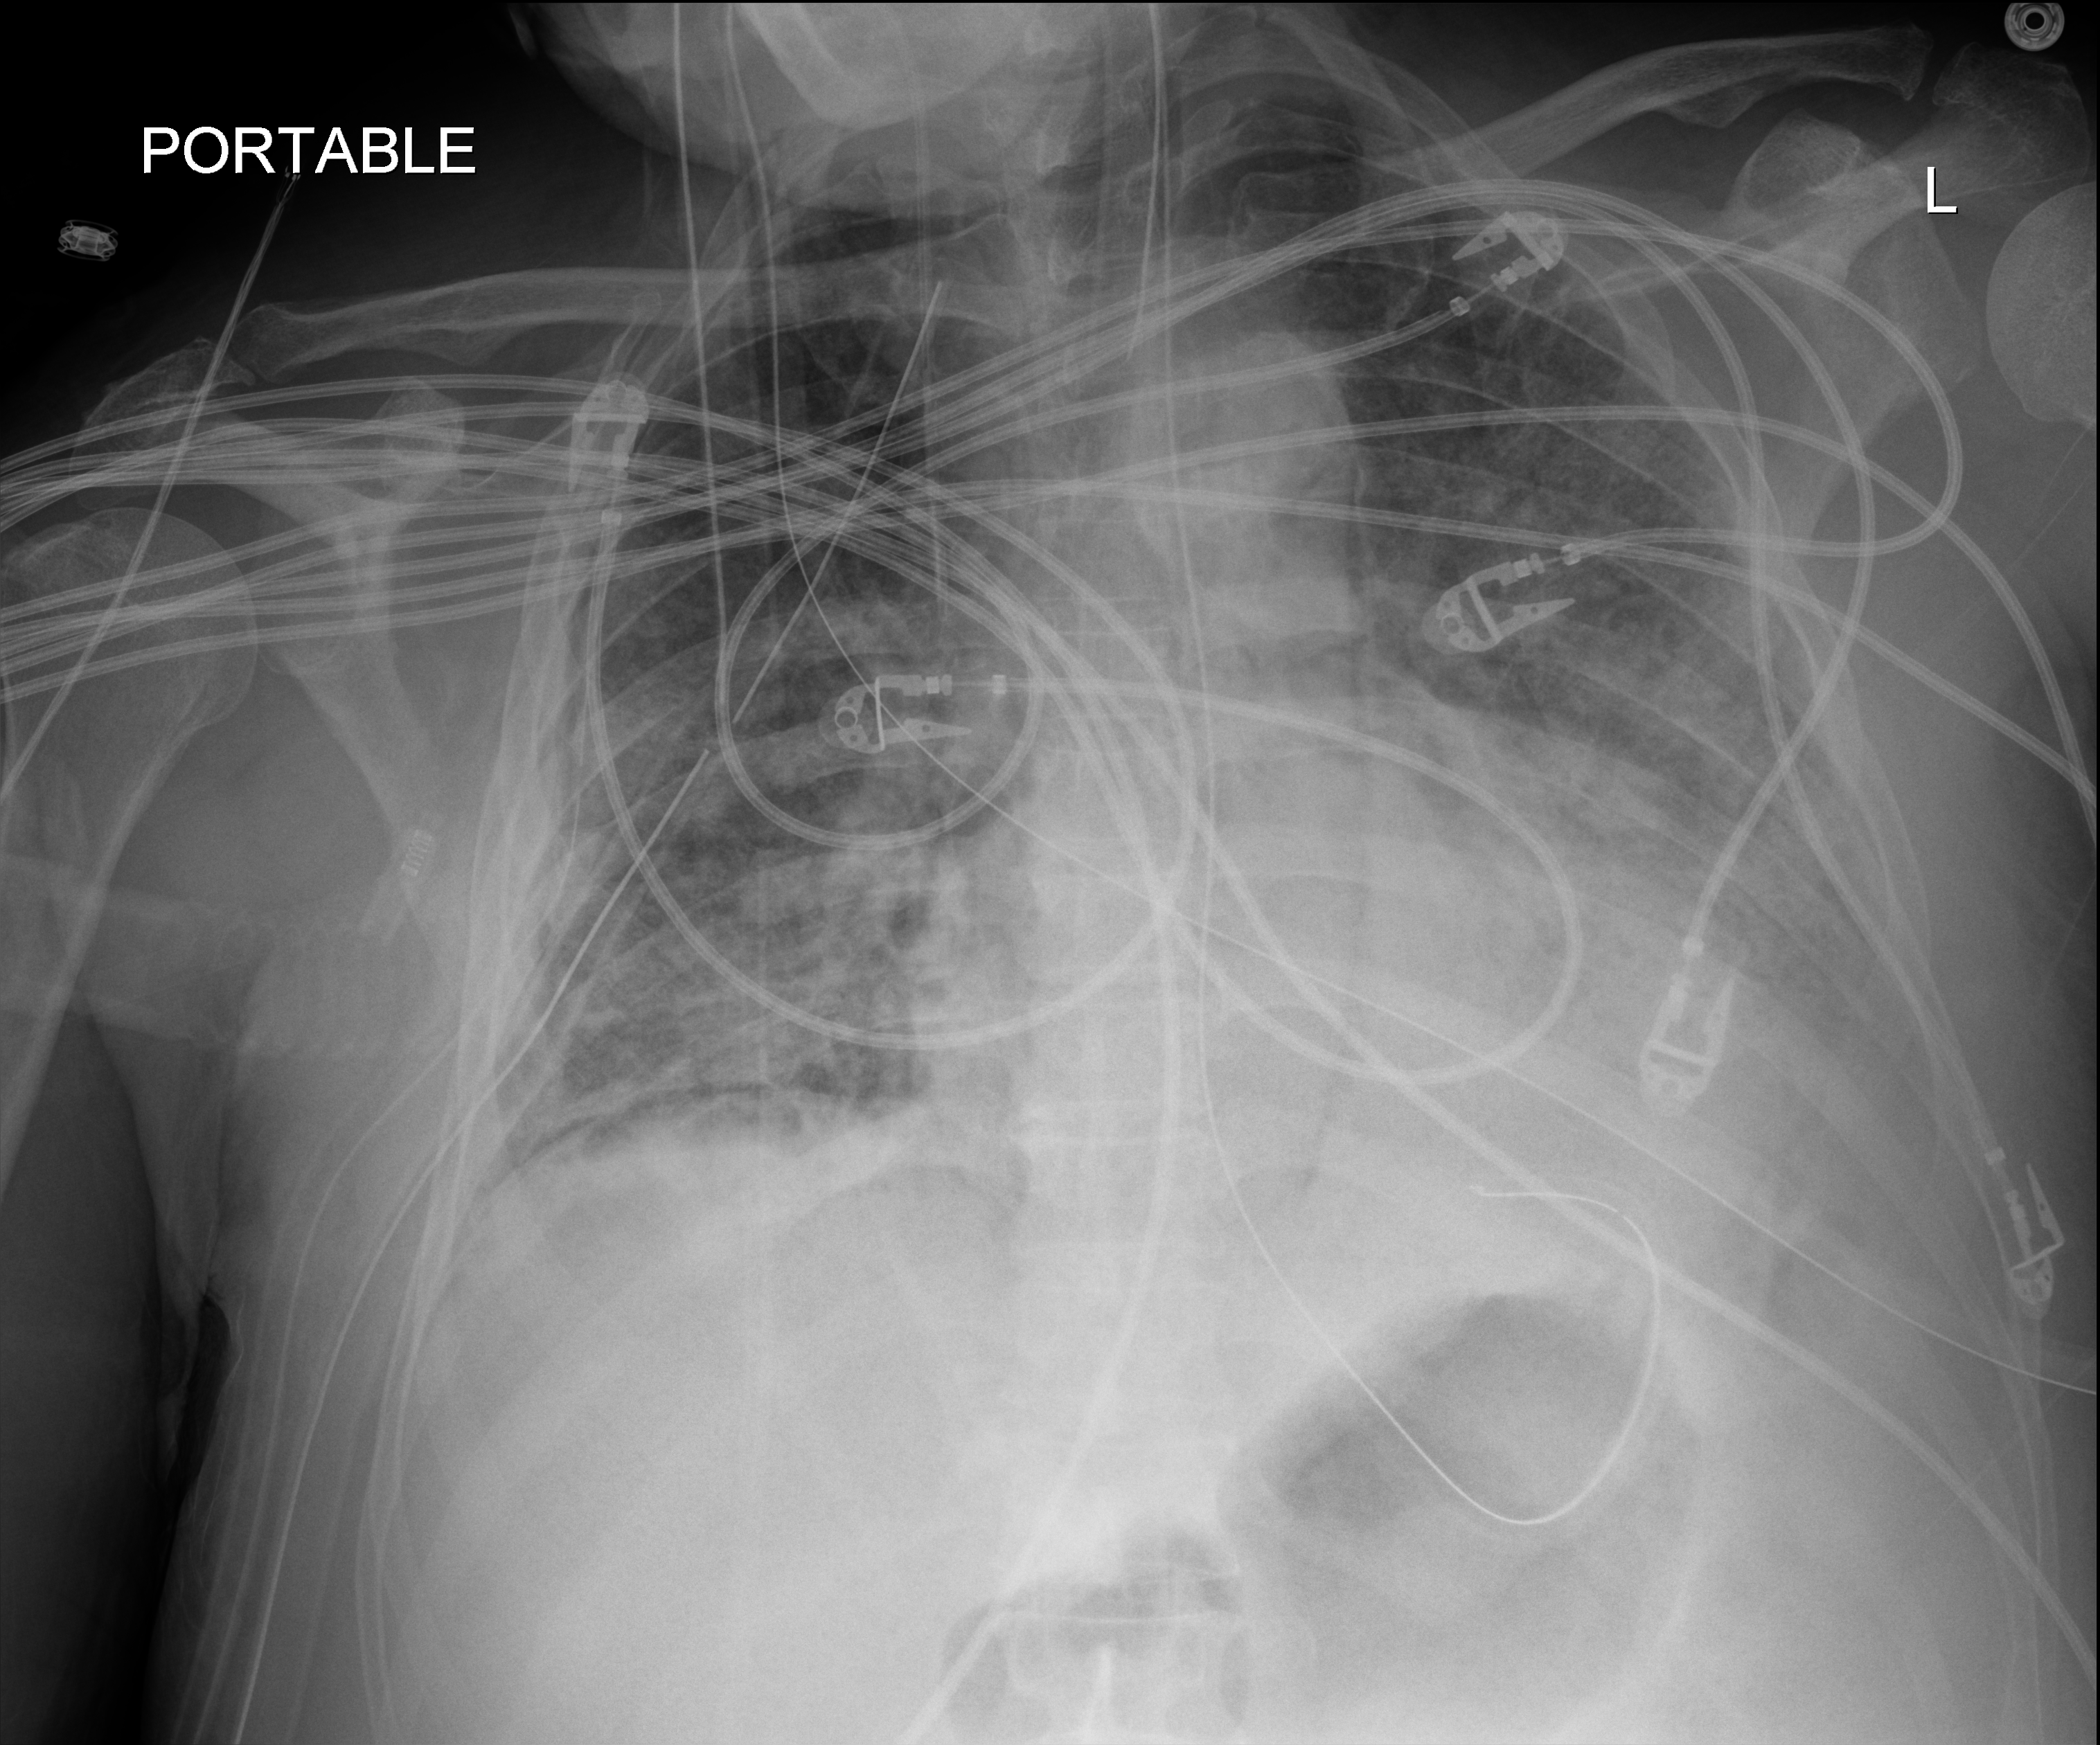
Chest X-ray (portable), anteroposterior (AP) projection. Male patient hospitalised with COVID-19, age 60–74 years.
From the hospital-stay record, not from the radiograph (when in the stay this image was taken is not recorded):
- mechanically ventilated during this hospital stay: yes
- diabetes (admission record): yes
- admitted to intensive care during this hospital stay: yes